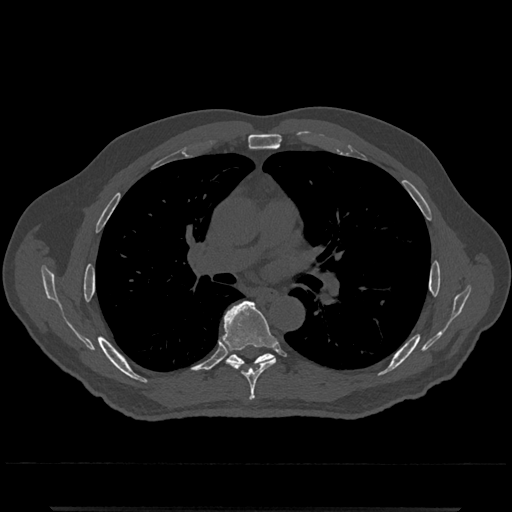
CT including the spine, one axial slice; slice 755 of 797 in the series (ordered by position); reconstruction kernel Br40s/3; 120 kVp; bone window (W 1800 / L 400 HU); 0.5 mm slice thickness; 512 × 512 image matrix, field of view 393 × 393 mm. Patient: male, 67 years. Case-level facts recorded for this patient, not image findings: primary cancer: prostate.
Structures marked on this image (semi-automatically segmented with operator editing):
- T6 vertebra: box from (x=223, y=300) to (x=276, y=401) px
- T7 vertebra: (x=228, y=353)–(x=273, y=366)